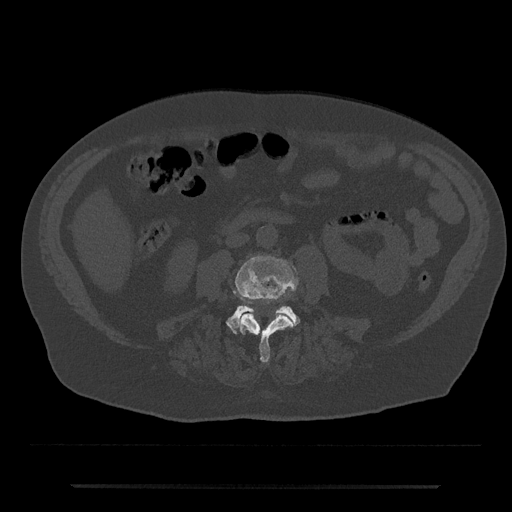
CT including the spine, one axial slice; slice 385 of 797 in the series (ordered by position); reconstruction kernel Br40s/3; bone window (W 1800 / L 400 HU); 512 × 512 image matrix. Patient: male, 80 years. From the clinical record (not read from this slice): primary cancer: prostate; vertebrae with lytic lesions (as recorded): L1, T11.
Annotated regions visible in this slice (semi-automatically segmented with operator editing):
- L3 vertebra: bounding box [x1, y1, x2, y2] px = [235, 255, 298, 363]
- L4 vertebra: [226, 305, 300, 334]